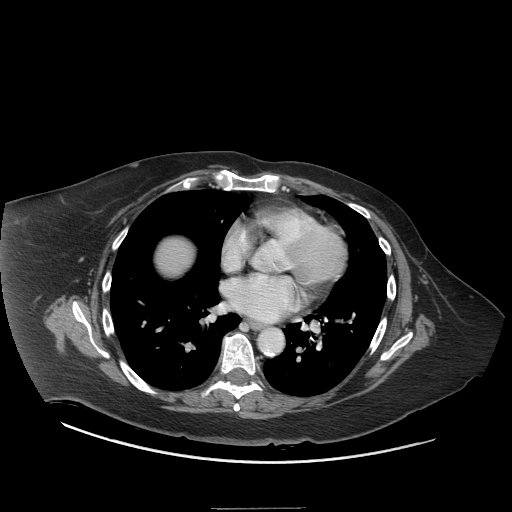
Contrast-enhanced abdominal CT (liver protocol), one axial slice. Reconstruction kernel STANDARD. 140 kVp. Soft-tissue window (W 400 / L 40 HU). 512 × 512 image matrix, field of view 440 × 440 mm. From the clinical record (not read from this slice): diagnosis: hepatocellular carcinoma (patient treated with transarterial chemoembolisation; whether this scan precedes or follows treatment is not stated here); TNM stage (as recorded): Stage-II.
Outlined on this slice (semi-automatically segmented with operator editing):
- liver parenchyma outside the tumour (the mass and vessels are separate outlines, so this box may not span the whole liver): box from (x=158, y=238) to (x=192, y=274) px